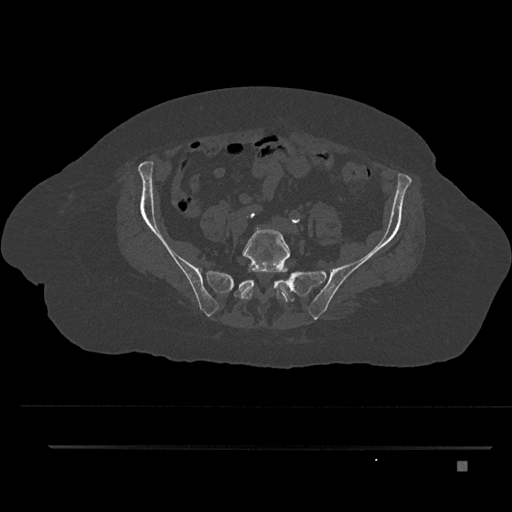
CT including the spine, one axial slice. Slice 23 of 797 in the series (ordered by position). 120 kVp. Bone window (W 1800 / L 400 HU). 0.5 mm slice thickness. 512 × 512 image matrix, field of view 437 × 437 mm. Female patient, age 76 years. Case-level facts recorded for this patient, not image findings: primary cancer: lung; vertebrae with lytic lesions (as recorded): T11, L3.
Outlined on this slice (semi-automatic segmentation, software-assisted and operator-edited):
- L5 vertebra: box from (x=241, y=227) to (x=291, y=302) px